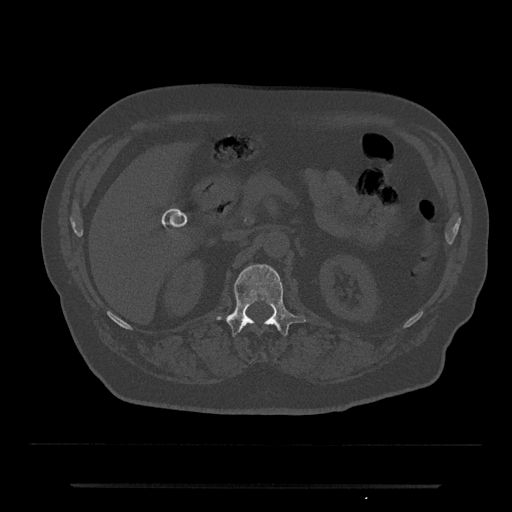
CT including the spine, one axial slice. Position 545 of 797 along the scan axis. Reconstruction kernel Br40s/3. Bone window (W 1800 / L 400 HU). 0.5 mm slice thickness. 512 × 512 image matrix, field of view 434 × 434 mm. Patient: male, 80 years. Case-level facts recorded for this patient, not image findings: primary cancer: prostate.
Structures marked on this image (semi-automatically segmented with operator editing):
- L1 vertebra: bounding box (x1, y1, x2, y2) in pixels: (216, 264, 306, 335)